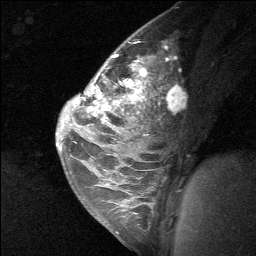
Breast MRI (dynamic contrast-enhanced), one sagittal slice. Position 43 of 64 along the scan axis. Dynamic contrast-enhanced study with each time point stored as its own series, time point 2 of 3 at this slice position (early post-contrast, ordered by acquisition time). 1.5 T. TE 4.8 ms, TR 27 ms. 2 mm slice thickness. 256 × 256 image matrix, field of view 180 × 180 mm. Female patient, age 26 years. Case-level facts recorded for this patient, not image findings: setting: breast cancer imaged before/during neoadjuvant chemotherapy; receptor status: HR-positive, HER2-negative.
Structures marked on this image (semi-automatically segmented with operator editing):
- analysis volume of interest (the breast-tissue region the enhancement analysis was run in; not a lesion): box from (x=86, y=43) to (x=166, y=138) px
- tumour enhancement mask (voxels above the 90 % enhancement threshold inside the analysis volume of interest): (x=91, y=55)–(x=147, y=118)